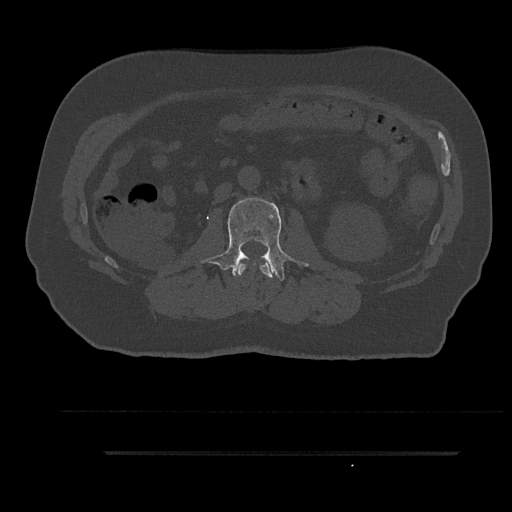
CT including the spine, one axial slice. Position 117 of 797 along the scan axis. Reconstruction kernel Br40s/3. Bone window (W 1800 / L 400 HU). 0.5 mm slice thickness. 512 × 512 image matrix. Male patient, age 63 years. Case-level facts recorded for this patient, not image findings: primary cancer: renal.
Outlined on this slice (semi-automatically segmented with operator editing):
- L1 vertebra: bounding box (x1, y1, x2, y2) in pixels: (238, 259, 274, 278)
- L2 vertebra: (200, 198, 308, 281)